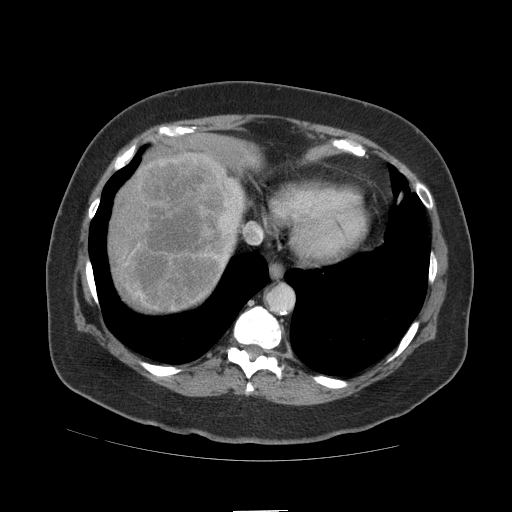
Contrast-enhanced abdominal CT (liver protocol), one axial slice; reconstruction kernel STANDARD; 140 kVp; soft-tissue window (W 400 / L 40 HU); 2.5 mm slice thickness; 512 × 512 image matrix. Case-level facts recorded for this patient, not image findings: diagnosis: hepatocellular carcinoma (patient treated with transarterial chemoembolisation; whether this scan precedes or follows treatment is not stated here); TNM stage (as recorded): Stage-IVB; Child-Pugh class: A; tumour differentiation: poorly differentiated; tumour nodularity: multinodular.
Outlined on this slice (semi-automatic segmentation, software-assisted and operator-edited):
- liver parenchyma outside the tumour (the mass and vessels are separate outlines, so this box may not span the whole liver): bounding box <108,136,258,310> (left, top, right, bottom; pixels)
- mass: <107,147,243,311>